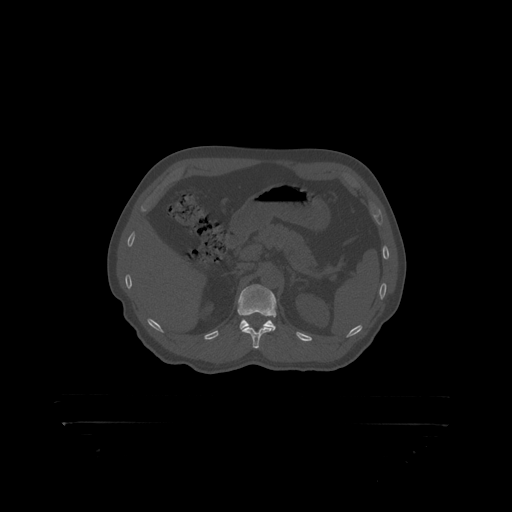
CT including the spine, one axial slice. Reconstruction kernel STANDARD. Bone window (W 1800 / L 400 HU). 512 × 512 image matrix, field of view 650 × 650 mm. Male patient, age 46 years. From the clinical record (not read from this slice): primary cancer: skin.
Structures marked on this image (semi-automatic segmentation, software-assisted and operator-edited):
- L1 vertebra: box from (x=238, y=285) to (x=277, y=317) px